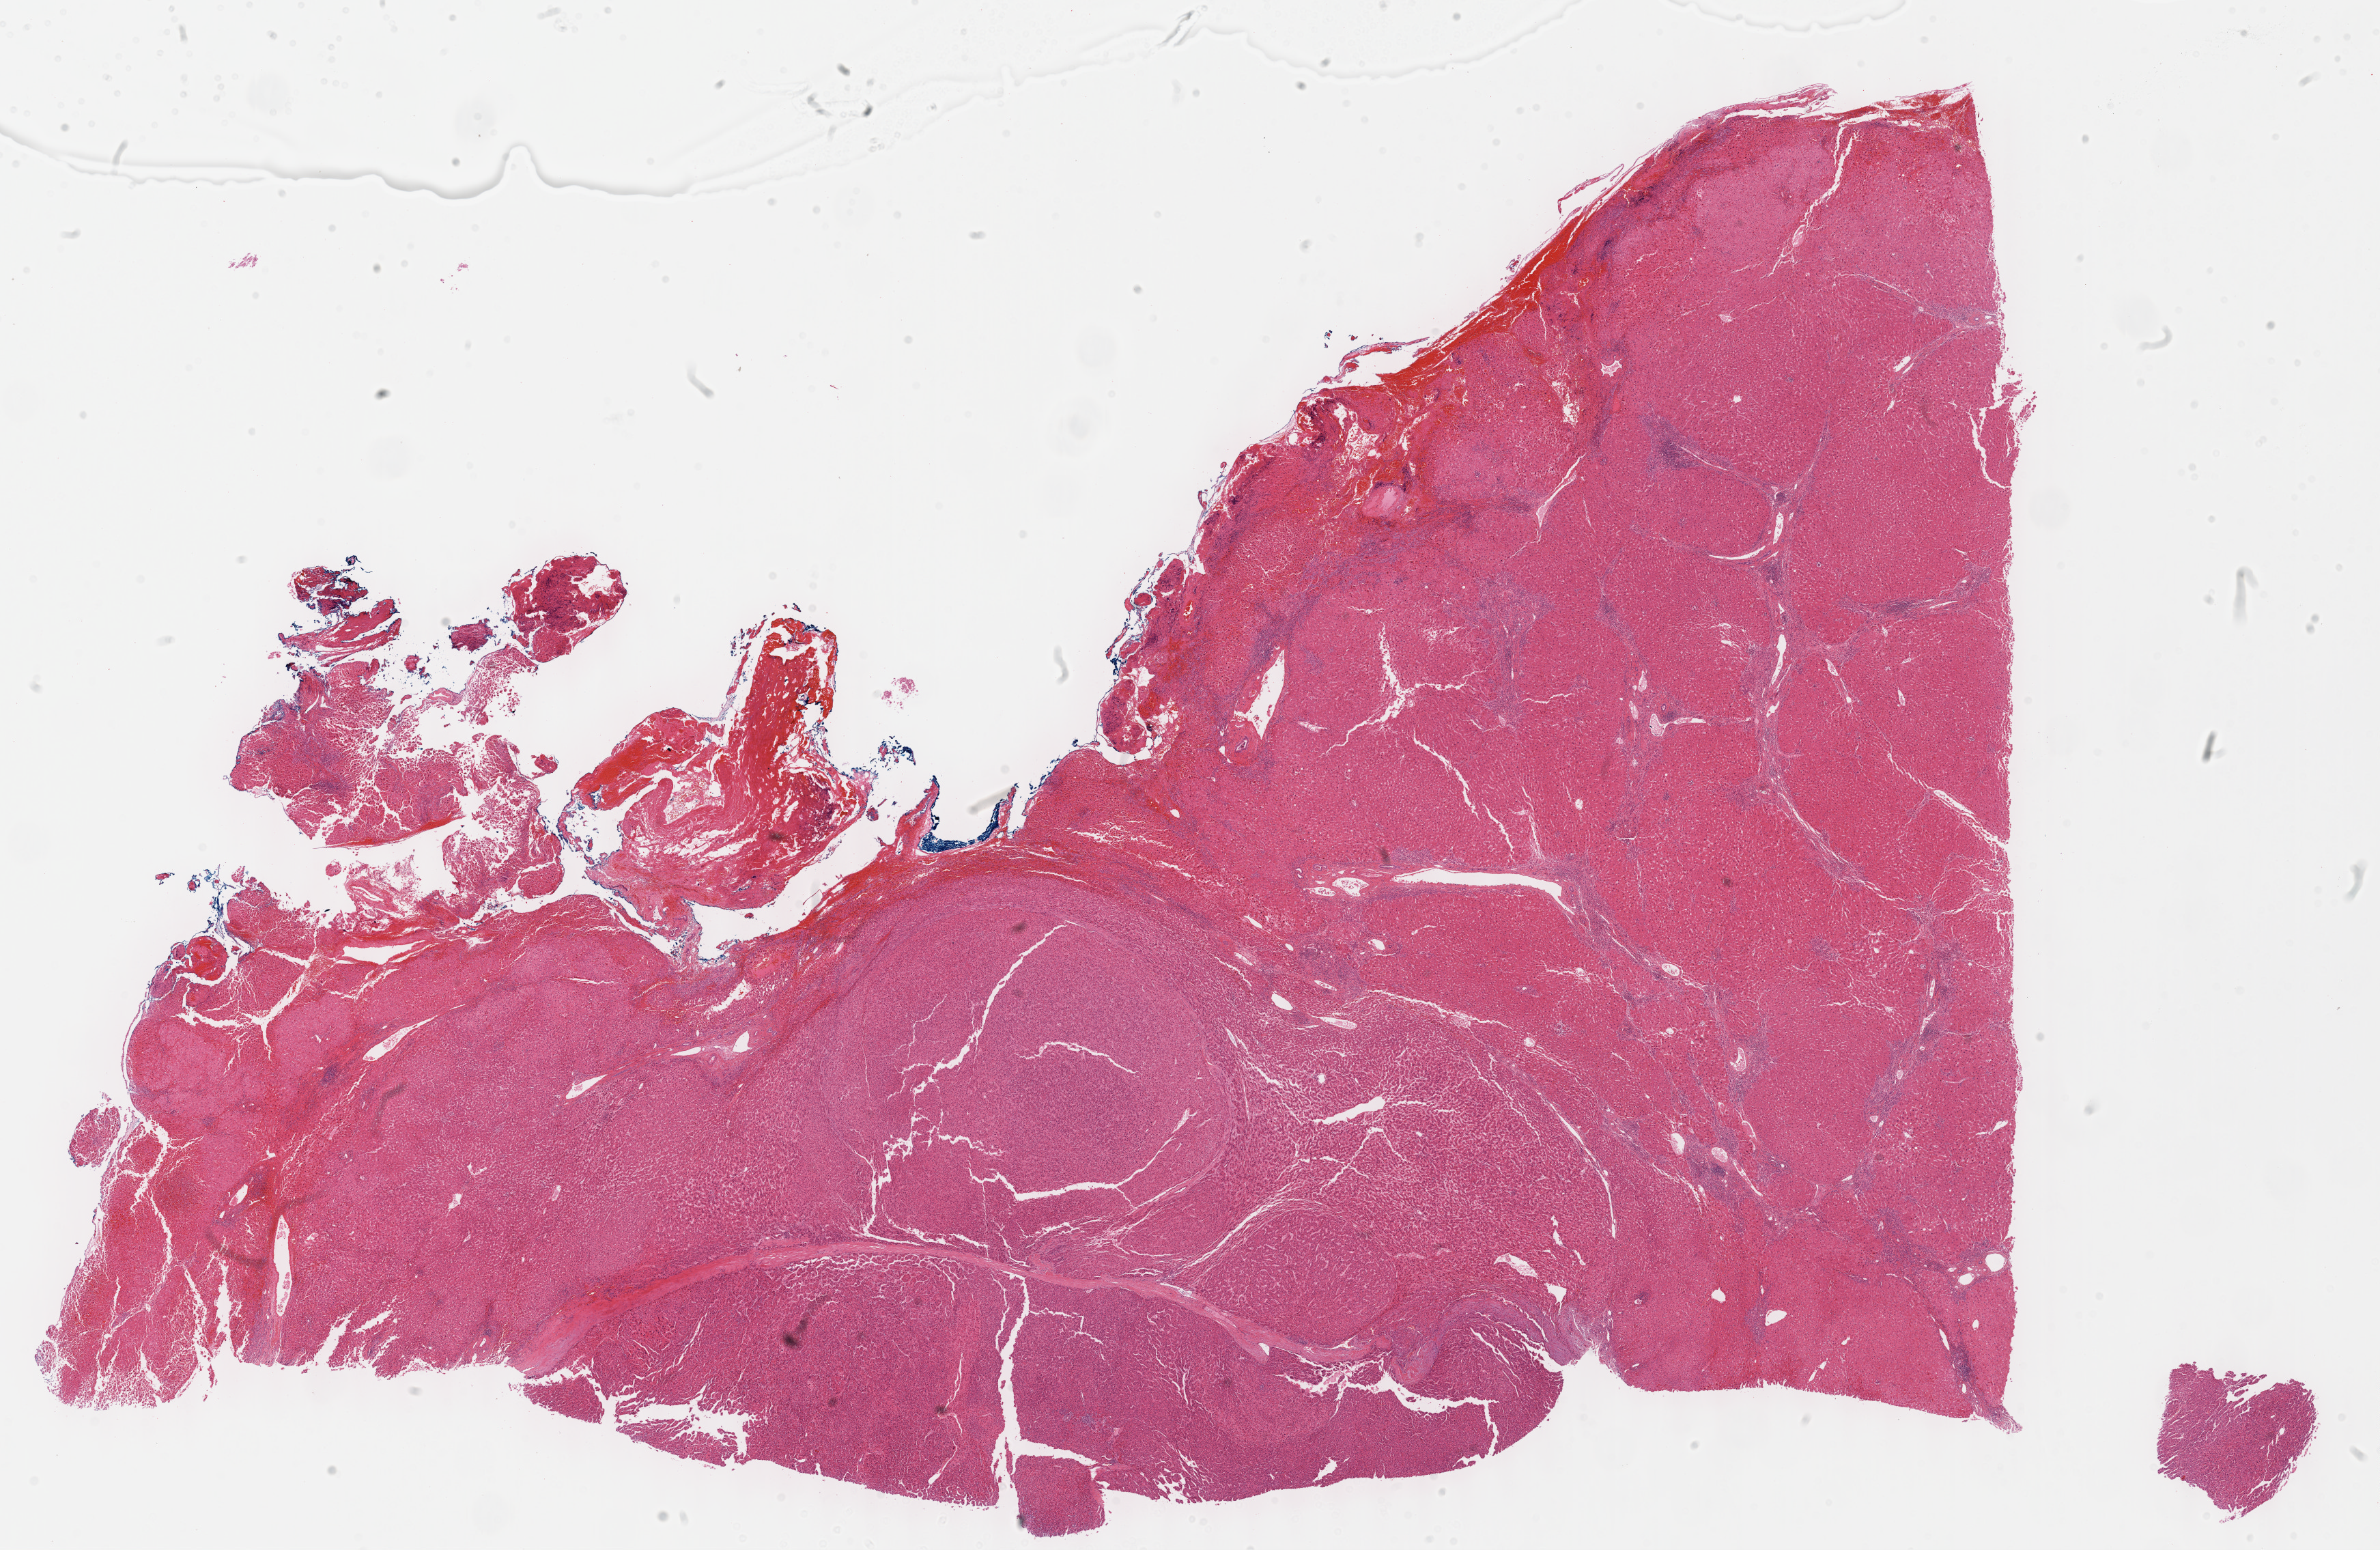
Whole-slide histology image, Hematoxylin and eosin (H&E) stained, shown as a low-resolution overview of the whole scanned area (about 28.2 x 18.3 mm, from a 40x scan); formalin-fixed paraffin-embedded (FFPE) diagnostic section; sample: primary tumour, liver. Patient: male, age at initial diagnosis 65 years. Histologic grade: G3 (poorly differentiated).
* histologic diagnosis: Hepatocellular carcinoma, NOS
* AJCC pathologic stage: I
* TNM: T1 N0 M0